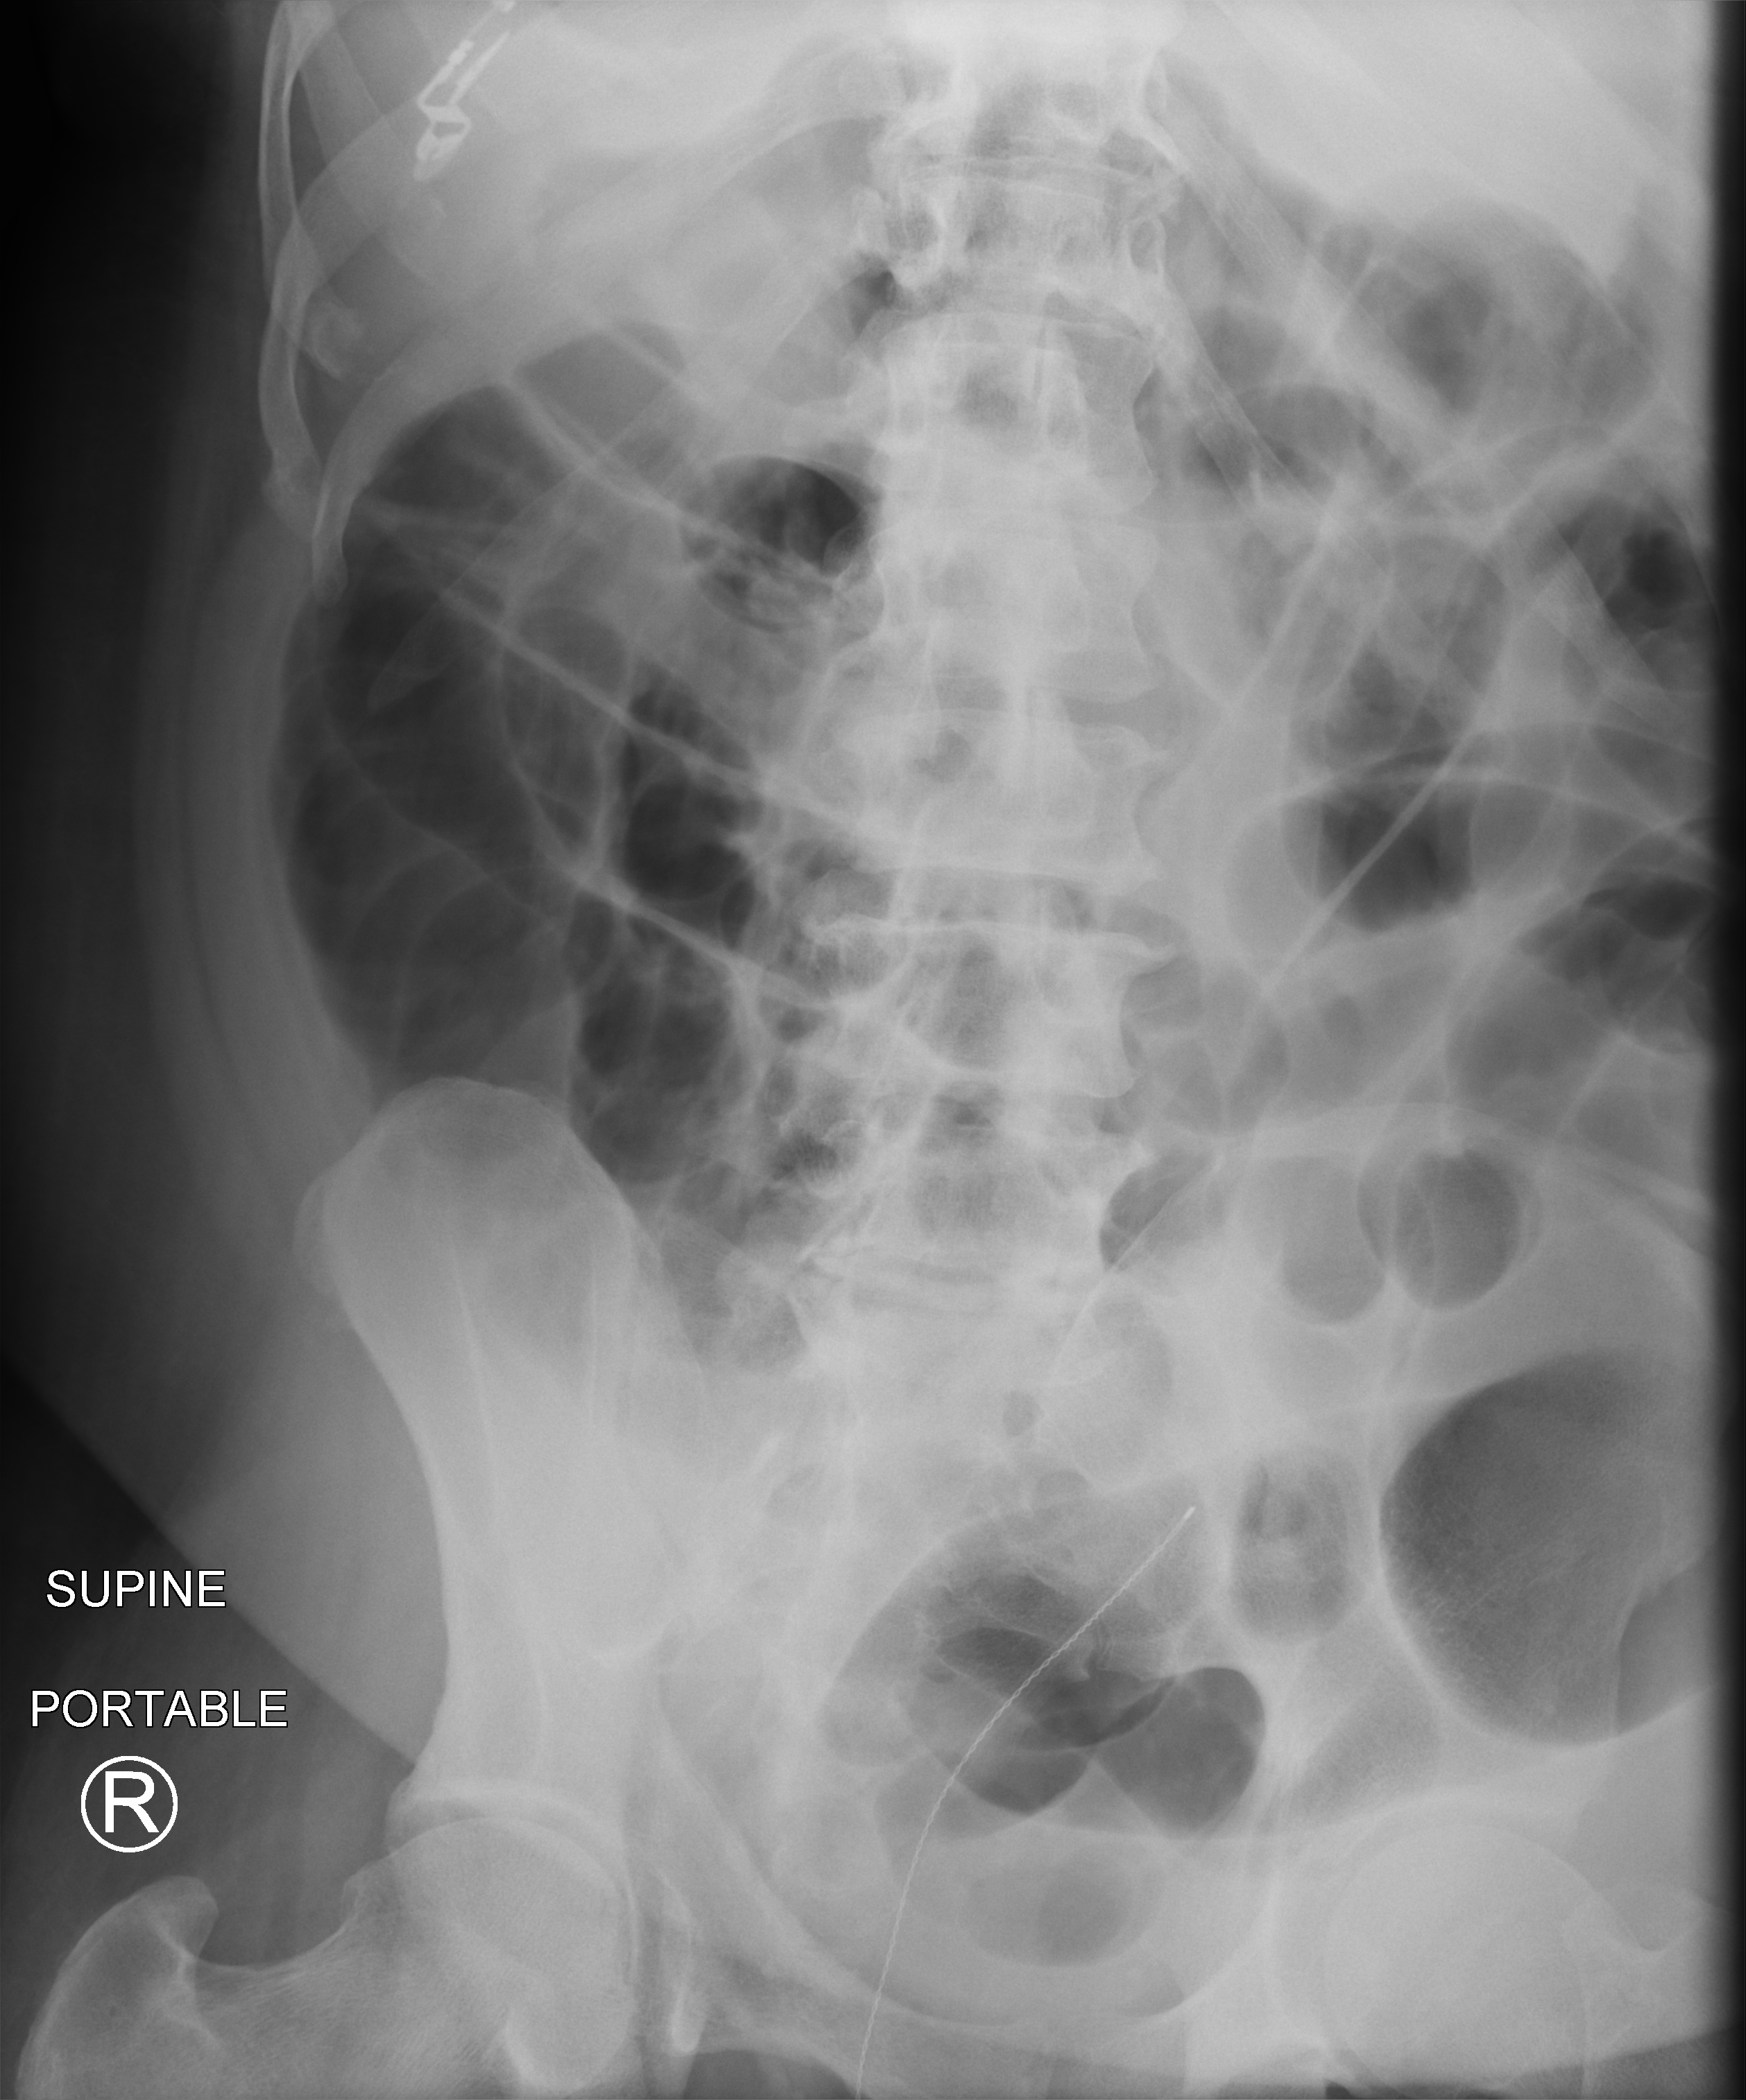
Abdomen X-ray (portable), anteroposterior (AP) projection. Male patient hospitalised with COVID-19, age 18–59 years.
Hospital-stay facts (about this admission, not read from this image; timing relative to this image not recorded): COPD (admission record): no; mechanically ventilated during this hospital stay: yes.